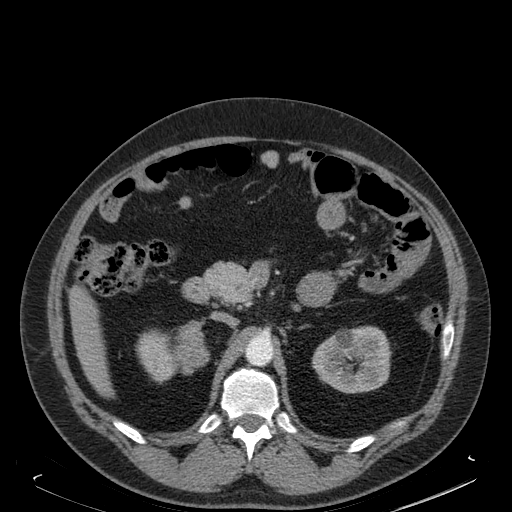
Contrast-enhanced abdominal CT, one axial slice. Slice 102 of 181 in the series (ordered by position). Soft-tissue window (W 400 / L 40 HU). 1.5 mm slice thickness. 512 × 512 image matrix, field of view 405 × 405 mm. Male patient. Case-level facts recorded for this patient, not image findings: diagnosis: adrenocortical carcinoma; tumour side: right adrenal; tumour size at pathology: 7.5 cm; Ki-67 index: 25 %; stage (as recorded): 4.
Outlined on this slice (semi-automatic segmentation, software-assisted and operator-edited):
- mass: bounding box (x1, y1, x2, y2) in pixels: (180, 322, 206, 365)